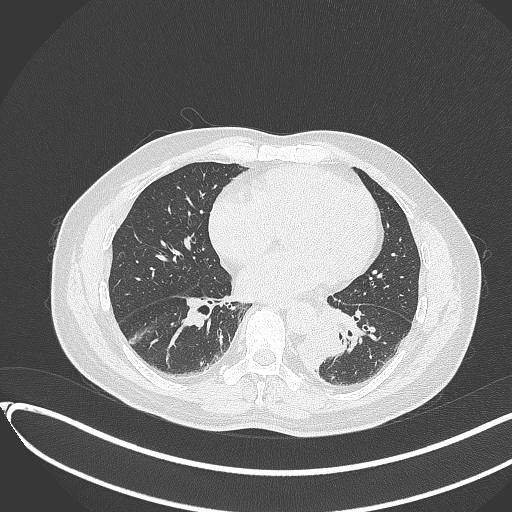
Chest CT, one axial slice; slice 135 of 417 in the series (ordered by position); reconstruction kernel B70f; lung window (W 1500 / L -600 HU); 512 × 512 image matrix. Male patient, age 54 years. From the clinical record (not read from this slice): clinical TNM (as recorded): T3 N0 M0.
Outlined on this slice (bounding box drawn by a radiologist):
- lung tumour (recorded histology: squamous cell carcinoma): bounding box <299,325,349,370> (left, top, right, bottom; pixels)